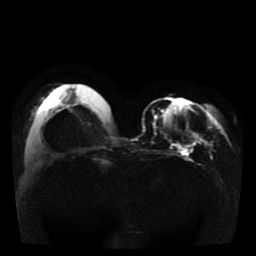
Breast MRI, one axial slice; slice 13 of 41 in the series (ordered by position); diffusion-weighted series; image 2 of 4 stored at this slice position (different b-values; order by instance number); 1.5 T; 5 mm slice thickness; 256 × 256 image matrix. Female patient.
Outlined on this slice (manually delineated by an expert):
- tumour on diffusion-weighted imaging: bounding box [x1, y1, x2, y2] px = [178, 133, 199, 148]